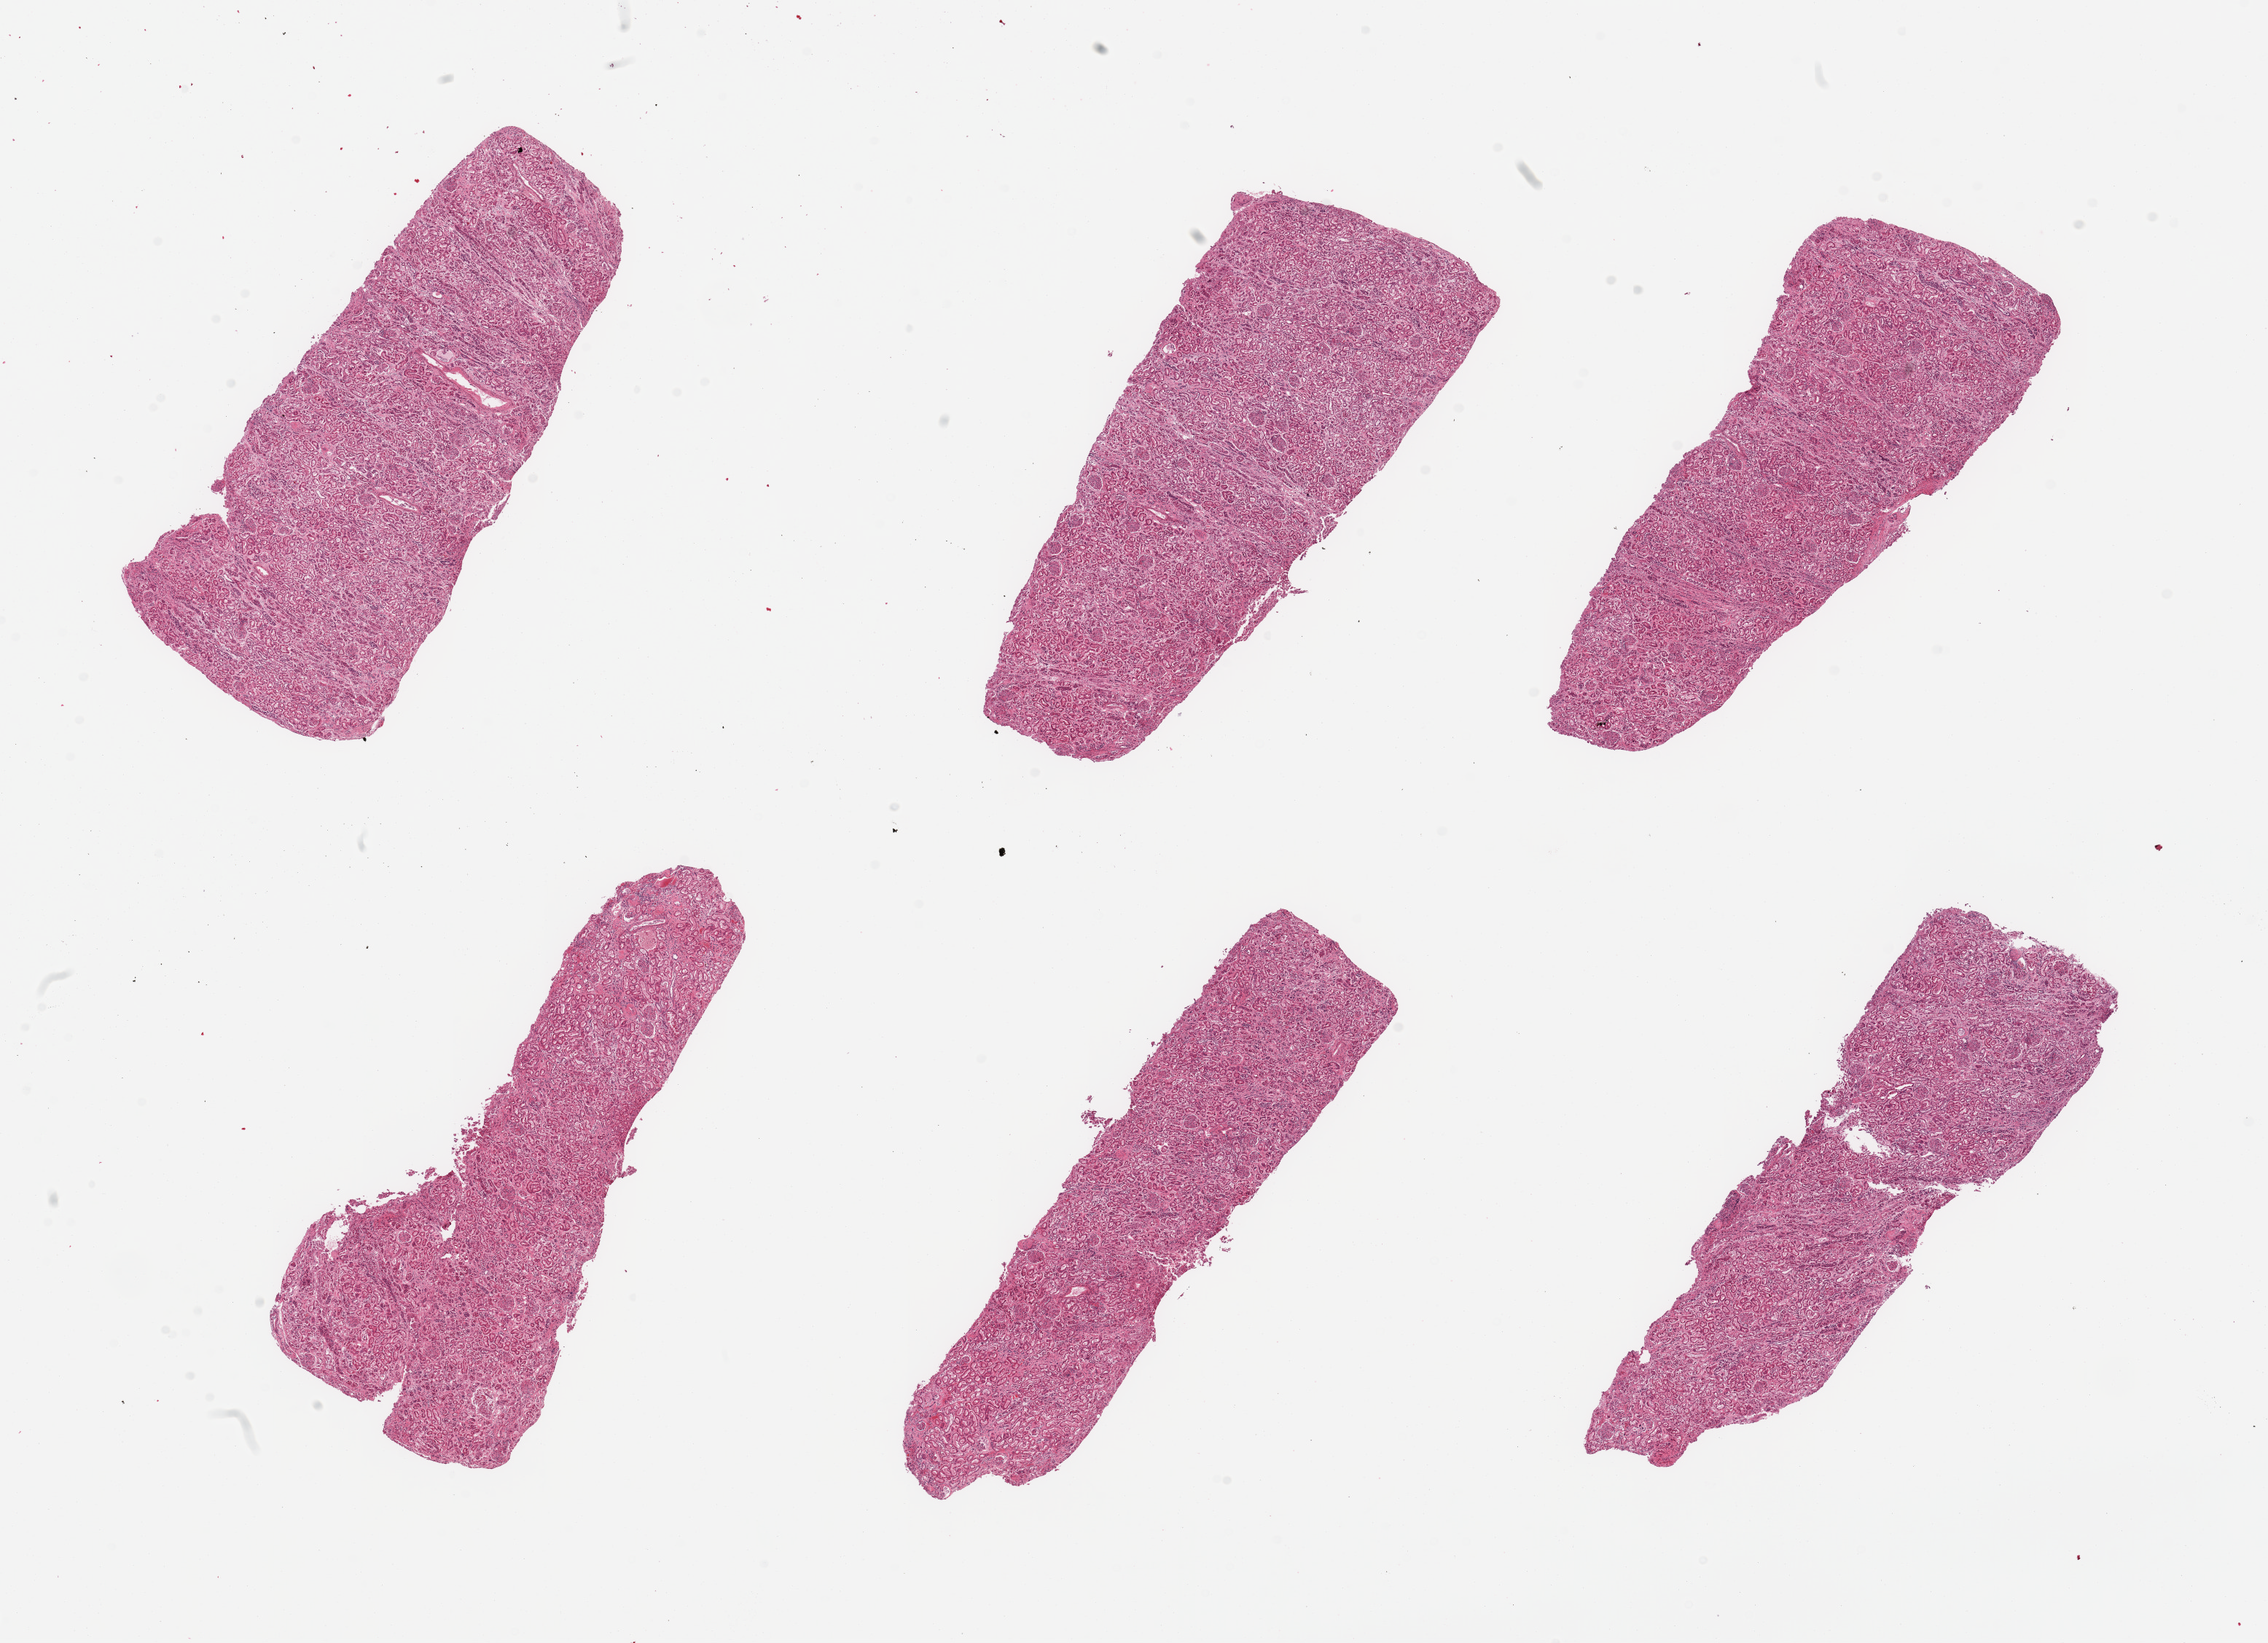
Haematoxylin and eosin whole-slide image, brightfield — whole scanned area (about 24.6 x 17.8 mm, from a 20x scan) shown as a low-resolution overview. PAXgene-fixed, paraffin-embedded tissue. Section of renal cortex (target tissue). Tissue donor sample. Female donor.
- pathologist's review note for this sample: 6 pieces; occasional sclerosed glomeruli and arteriolar changes